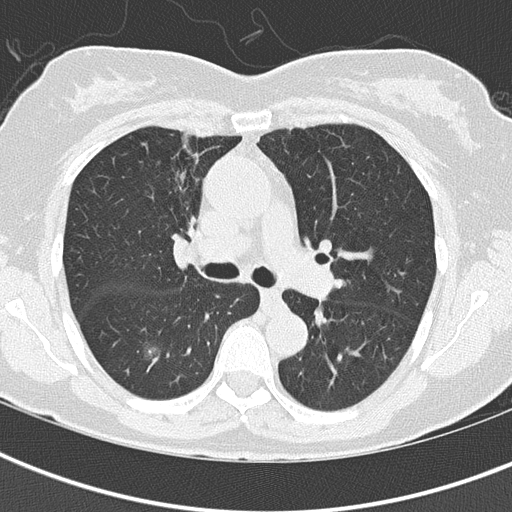
Chest CT (low-dose screening protocol), one axial image; baseline screening round; lung window (W 1500 / L -600 HU); lung (sharp) reconstruction kernel (B50f); 512 × 512 image matrix, field of view 290 × 290 mm. Female, age 68 years at enrolment.
Expert-annotated lung lesion, bounding box <122,325,180,376> (left, top, right, bottom; pixels). The exam's reader record, not a measurement of the box and not confirmed to be the same lesion: non-calcified nodule or mass ≥4 mm, right lower lobe, 19 × 17 mm, spiculated (stellate) margins, ground glass attenuation. Later outcome: lung cancer diagnosed 40 days after this screen — bronchiolo-alveolar adenocarcinoma, NOS, right lower lobe, well differentiated (G1), stage IA (AJCC 6th edition), 15 mm at pathology.